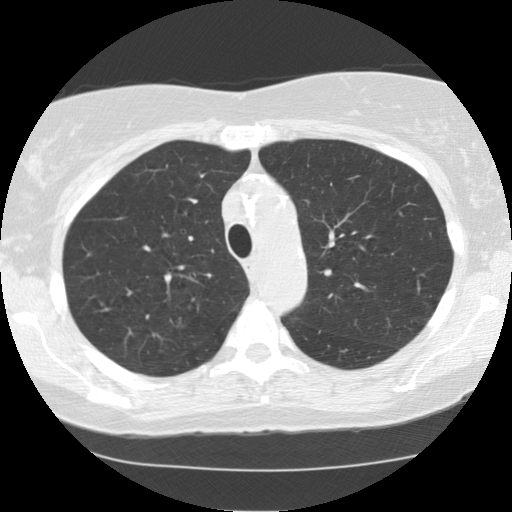
Axial slice from a low-dose chest CT screening exam, baseline screening round, lung window (W 1500 / L -600 HU), 2.5 mm slice thickness. Female participant, aged 72 years at enrolment. Former smoker at enrolment.
Expert reader's lesion annotation, bounding box <155,300,195,344> (left, top, right, bottom; pixels). The screening reader recorded 5 non-calcified nodules or masses ≥4 mm on this exam; which of them this box marks is not recorded. Lung cancer was diagnosed 812 days after this screen (after the third annual screen): bronchiolo-alveolar adenocarcinoma, NOS, right upper lobe, well differentiated (G1), stage IA (AJCC 6th edition), 8 mm at pathology.